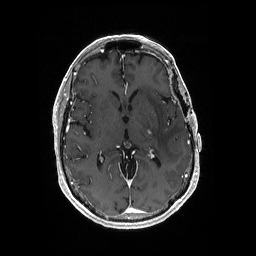
Brain MRI from a brain-tumour surgery series, one axial slice. Position 102 of 176 along the scan axis. T1-weighted post-contrast. 1 mm slice thickness. 256 × 256 image matrix. Case-level facts recorded for this patient, not image findings: histopathology: Glioblastoma; WHO grade: 4; IDH mutation: no; tumour location: Left Medial Temporal.
Annotated regions visible in this slice (expert manual segmentation):
- tumour: box from (x=147, y=130) to (x=151, y=134) px